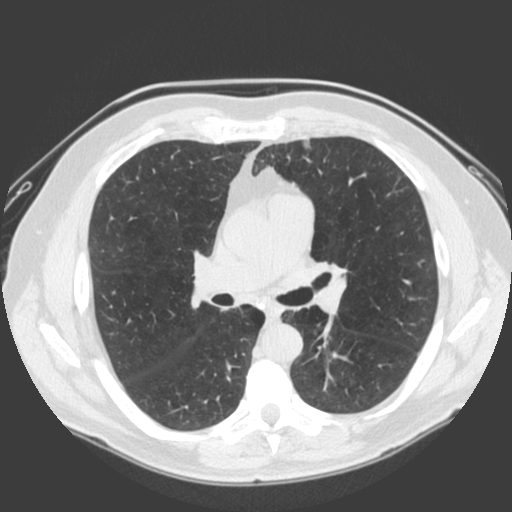
Low-dose screening chest CT, one axial slice; slice 107 of 185 in the series (ordered by position); 120 kVp; lung window (W 1500 / L -600 HU); 2 mm slice thickness; 512 × 512 image matrix, field of view 360 × 360 mm.
Annotated regions visible in this slice (outlined manually by an expert reader):
- lesion 1 (tumor, lower lobe of left lung): bounding box <304,140,310,148> (left, top, right, bottom; pixels)